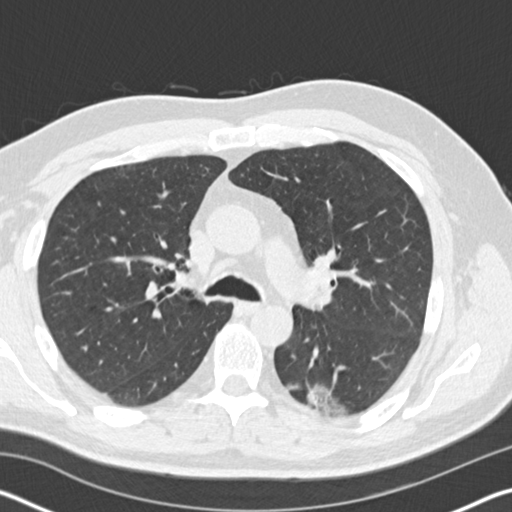
Low-dose screening chest CT, one axial slice. Position 112 of 178 along the scan axis. Lung window (W 1500 / L -600 HU). 2 mm slice thickness. 512 × 512 image matrix, field of view 340 × 340 mm.
Annotated regions visible in this slice (manually delineated by an expert):
- lesion 1 (tumor, lower lobe of left lung): bounding box <307,384,346,415> (left, top, right, bottom; pixels)